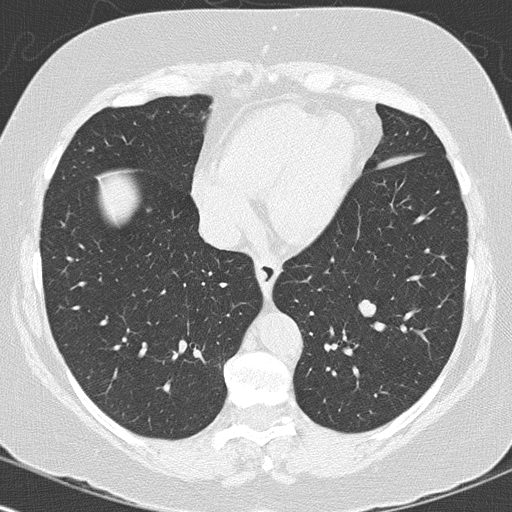
Low-dose screening chest CT, one axial slice. Slice 49 of 144 in the series (ordered by position). Lung window (W 1500 / L -600 HU). 2 mm slice thickness. 512 × 512 image matrix.
Annotated regions visible in this slice (manually delineated by an expert):
- lesion 1 (tumor, lower lobe of left lung): box from (x=358, y=299) to (x=376, y=317) px